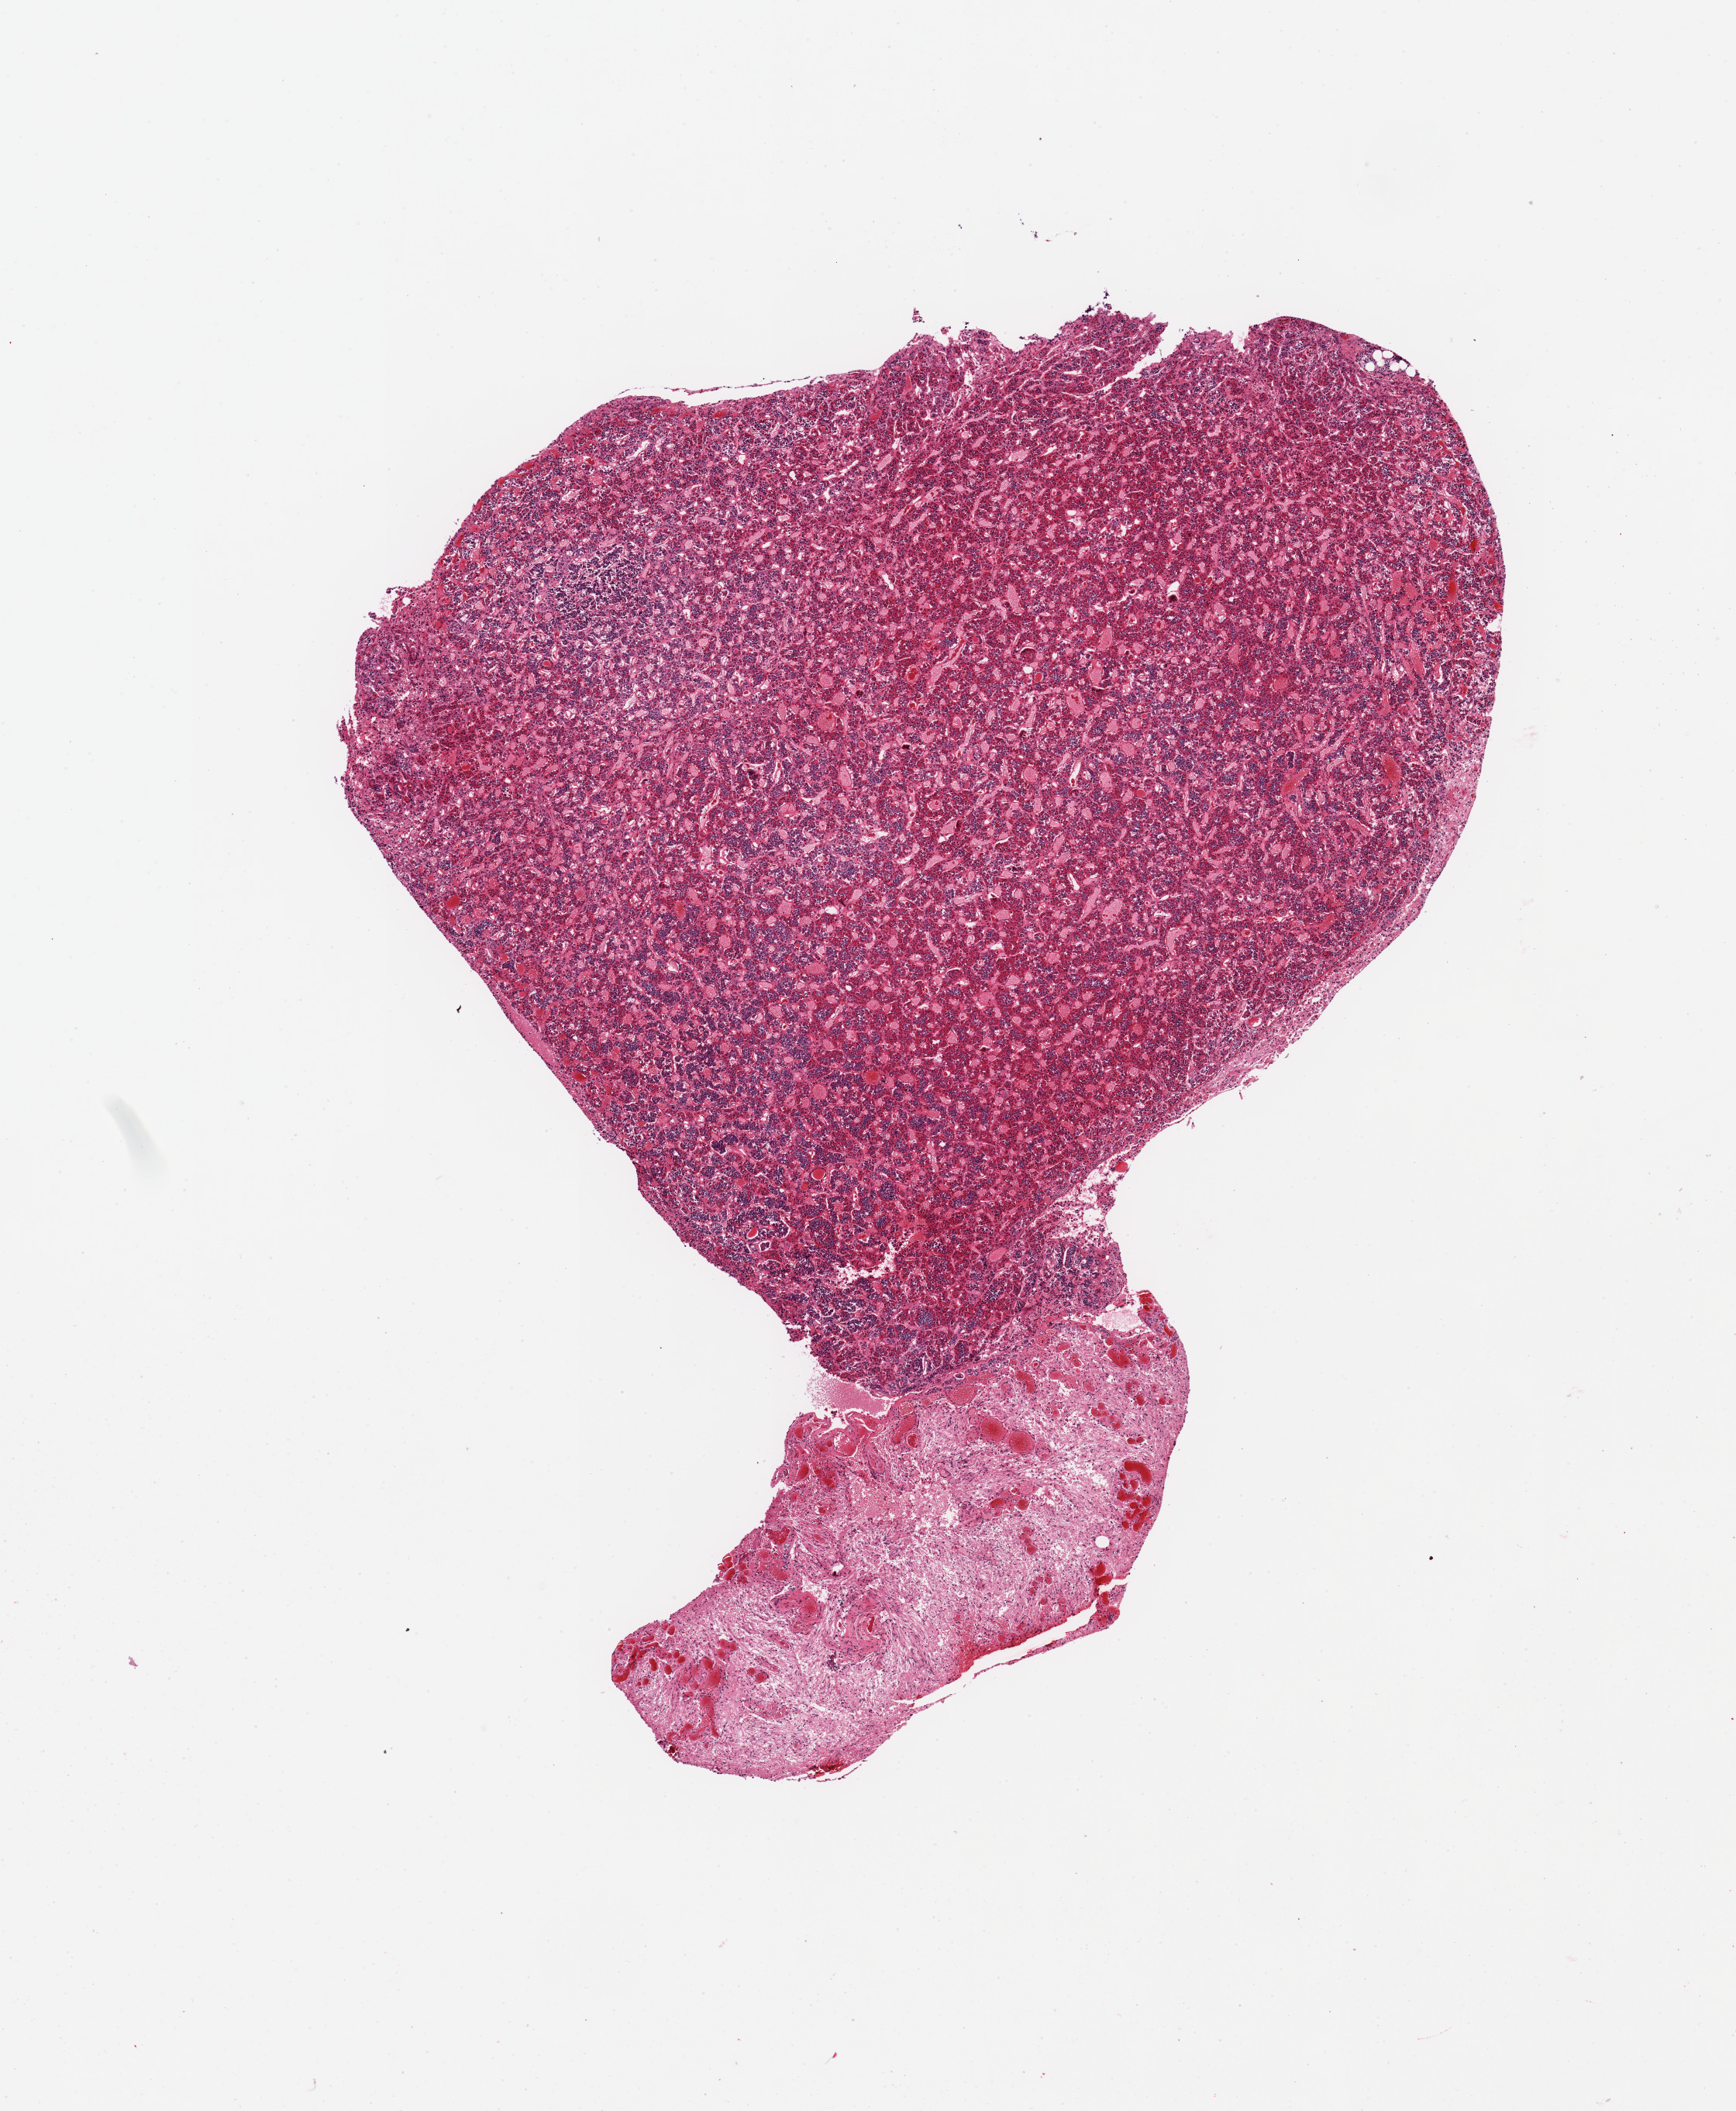
H&E whole-slide image, whole scanned area (about 8.9 x 10.8 mm, from a 20x scan) shown as a low-resolution overview, PAXgene-fixed, paraffin-embedded tissue, target tissue: pituitary, donor tissue sample.
- reviewer comment on this tissue sample: 1 piece, ~80% adenohypophysis; ~20% neurohypophysis, 3.5 x1.5mm nubbin